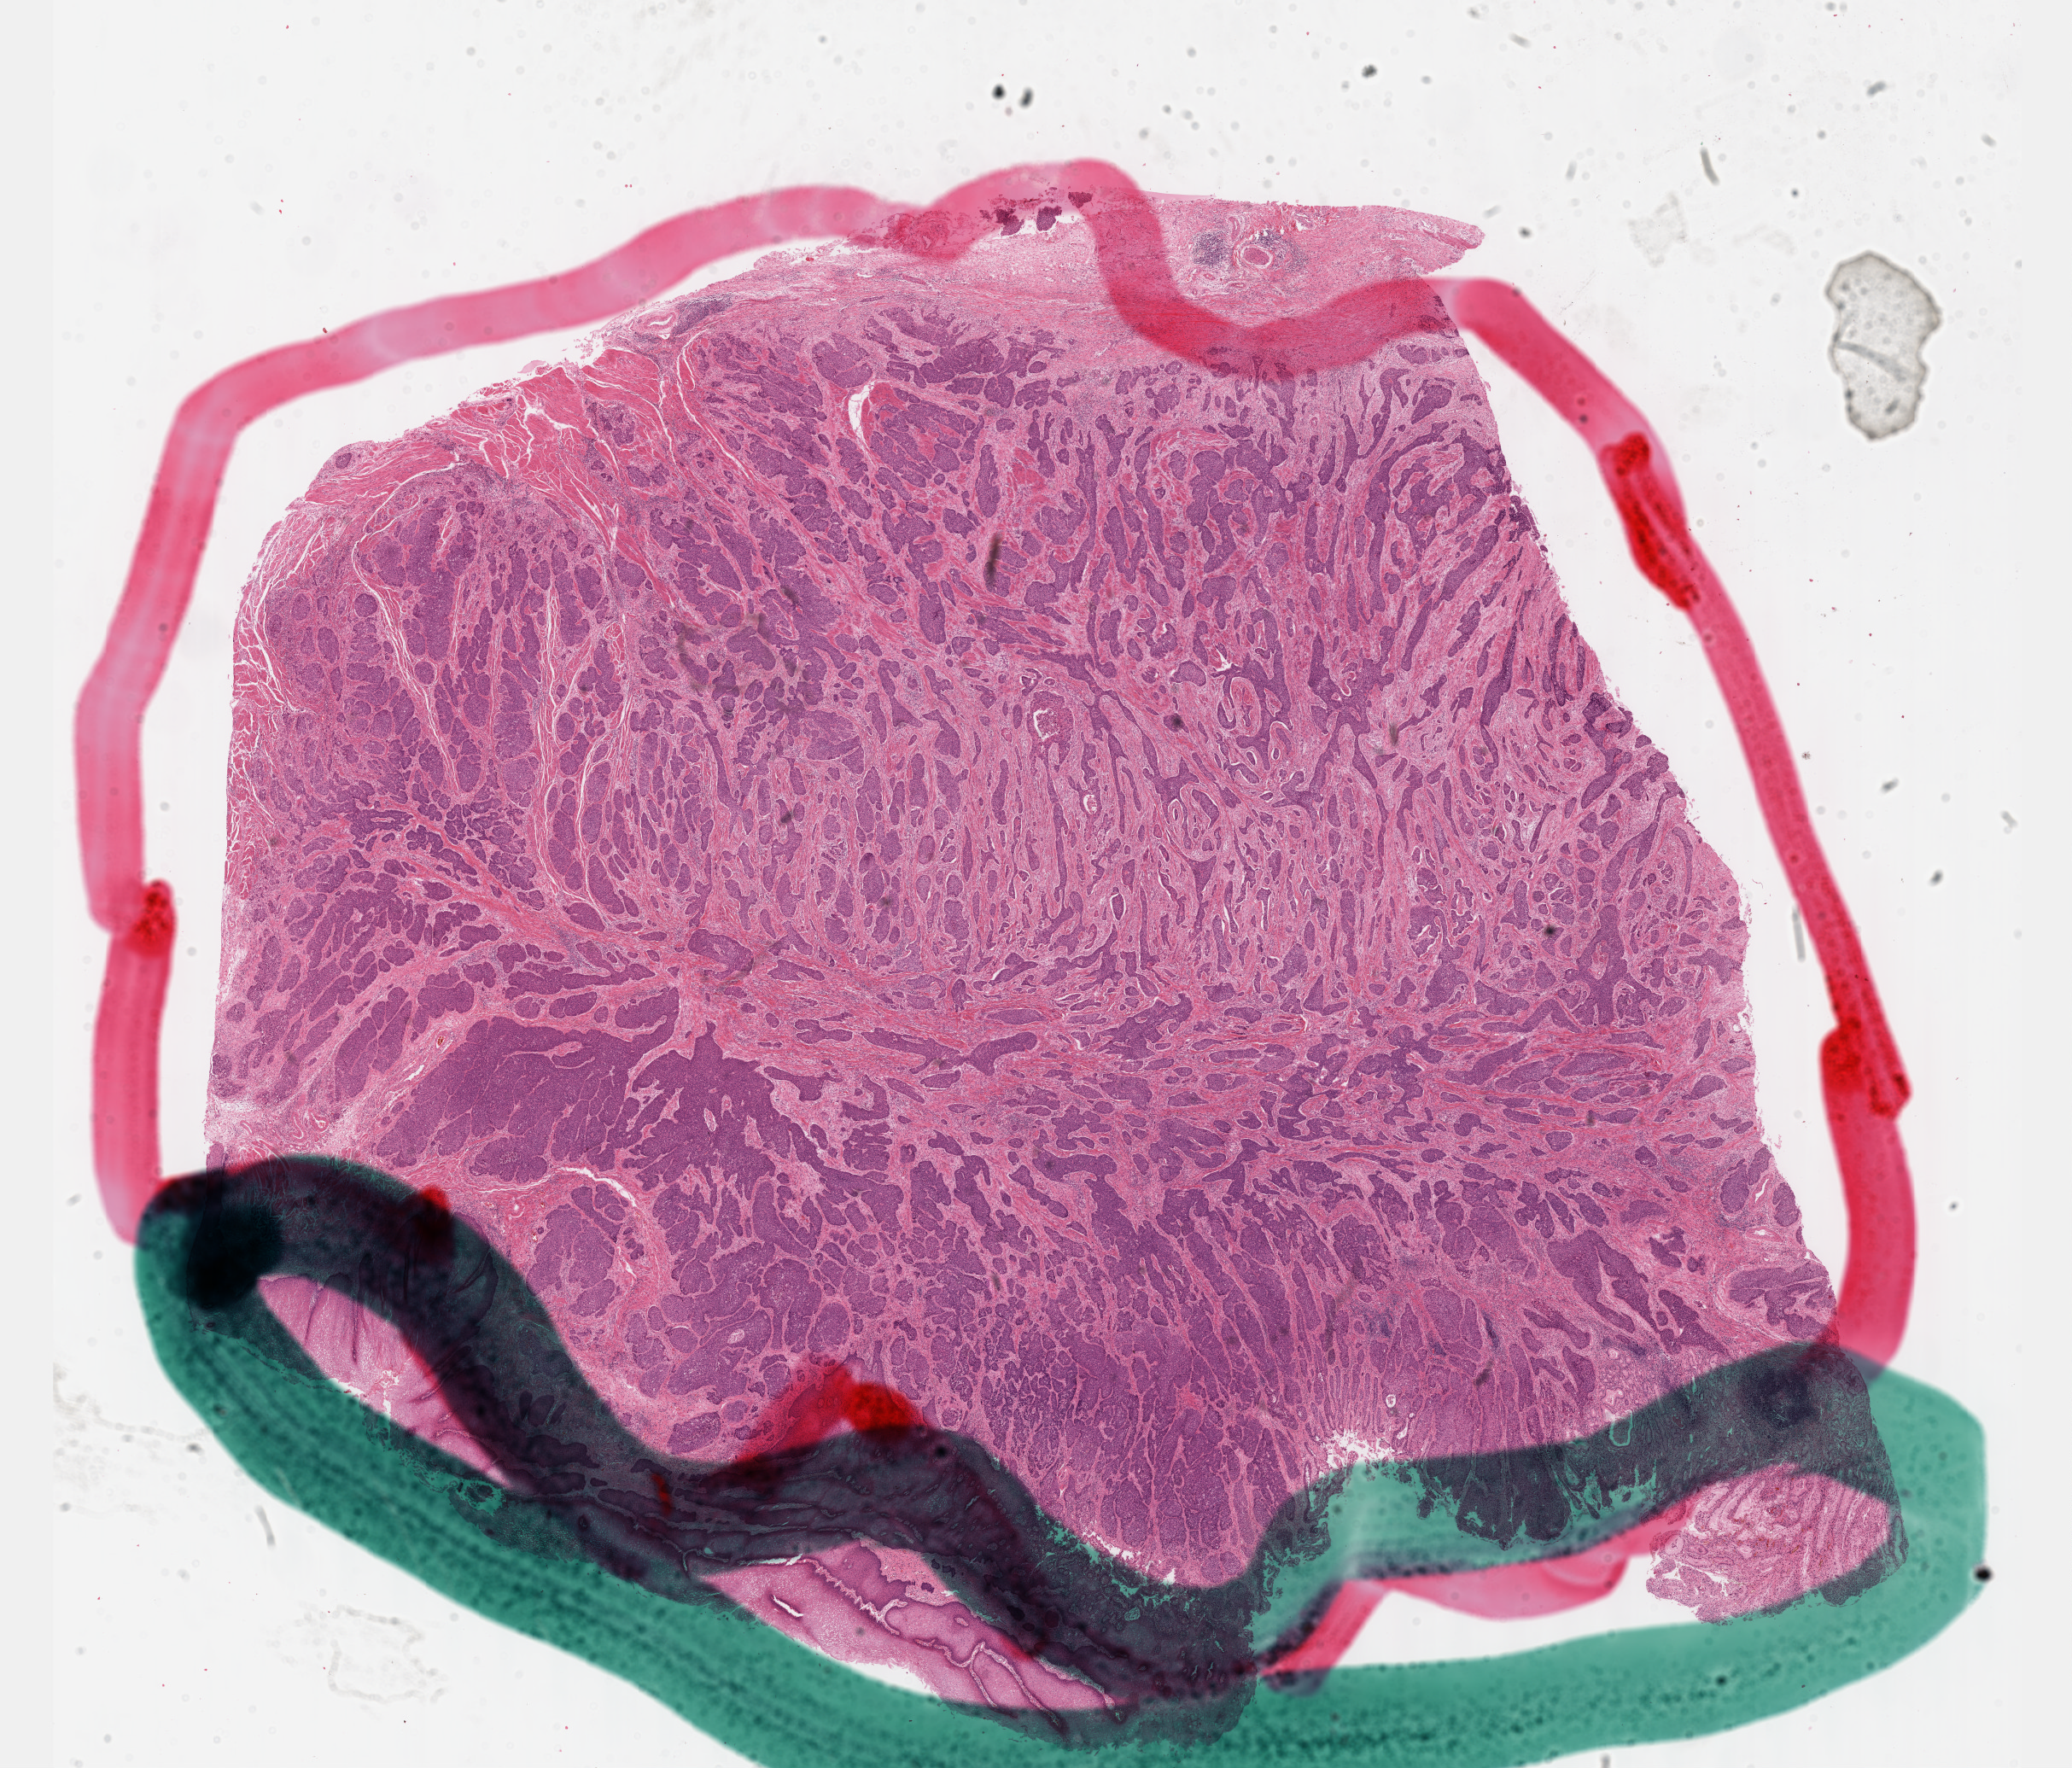
Digitized Hematoxylin and eosin (H&E) stained tissue section (whole slide), low-resolution overview of the scanned area, about 19.6 x 16.7 mm (acquisition: 40x scan); FFPE section; primary tumour sample from the esophagus. Male, age 62 years at initial diagnosis. Histologic grade: G3 (poorly differentiated).
- AJCC pathologic stage: IIIB (7th edition)
- TNM: T3 N2 M0
- histologic diagnosis: Squamous cell carcinoma, NOS (lower third of esophagus)